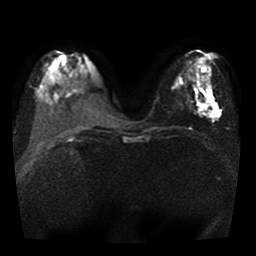
Breast MRI, one axial slice. Position 15 of 41 along the scan axis. Diffusion-weighted series; image 2 of 4 stored at this slice position (different b-values; order by instance number). 1.5 T. 5 mm slice thickness. 256 × 256 image matrix, field of view 330 × 330 mm. Female patient.
Outlined on this slice (expert manual segmentation):
- tumour on diffusion-weighted imaging: bounding box <208,98,220,118> (left, top, right, bottom; pixels)